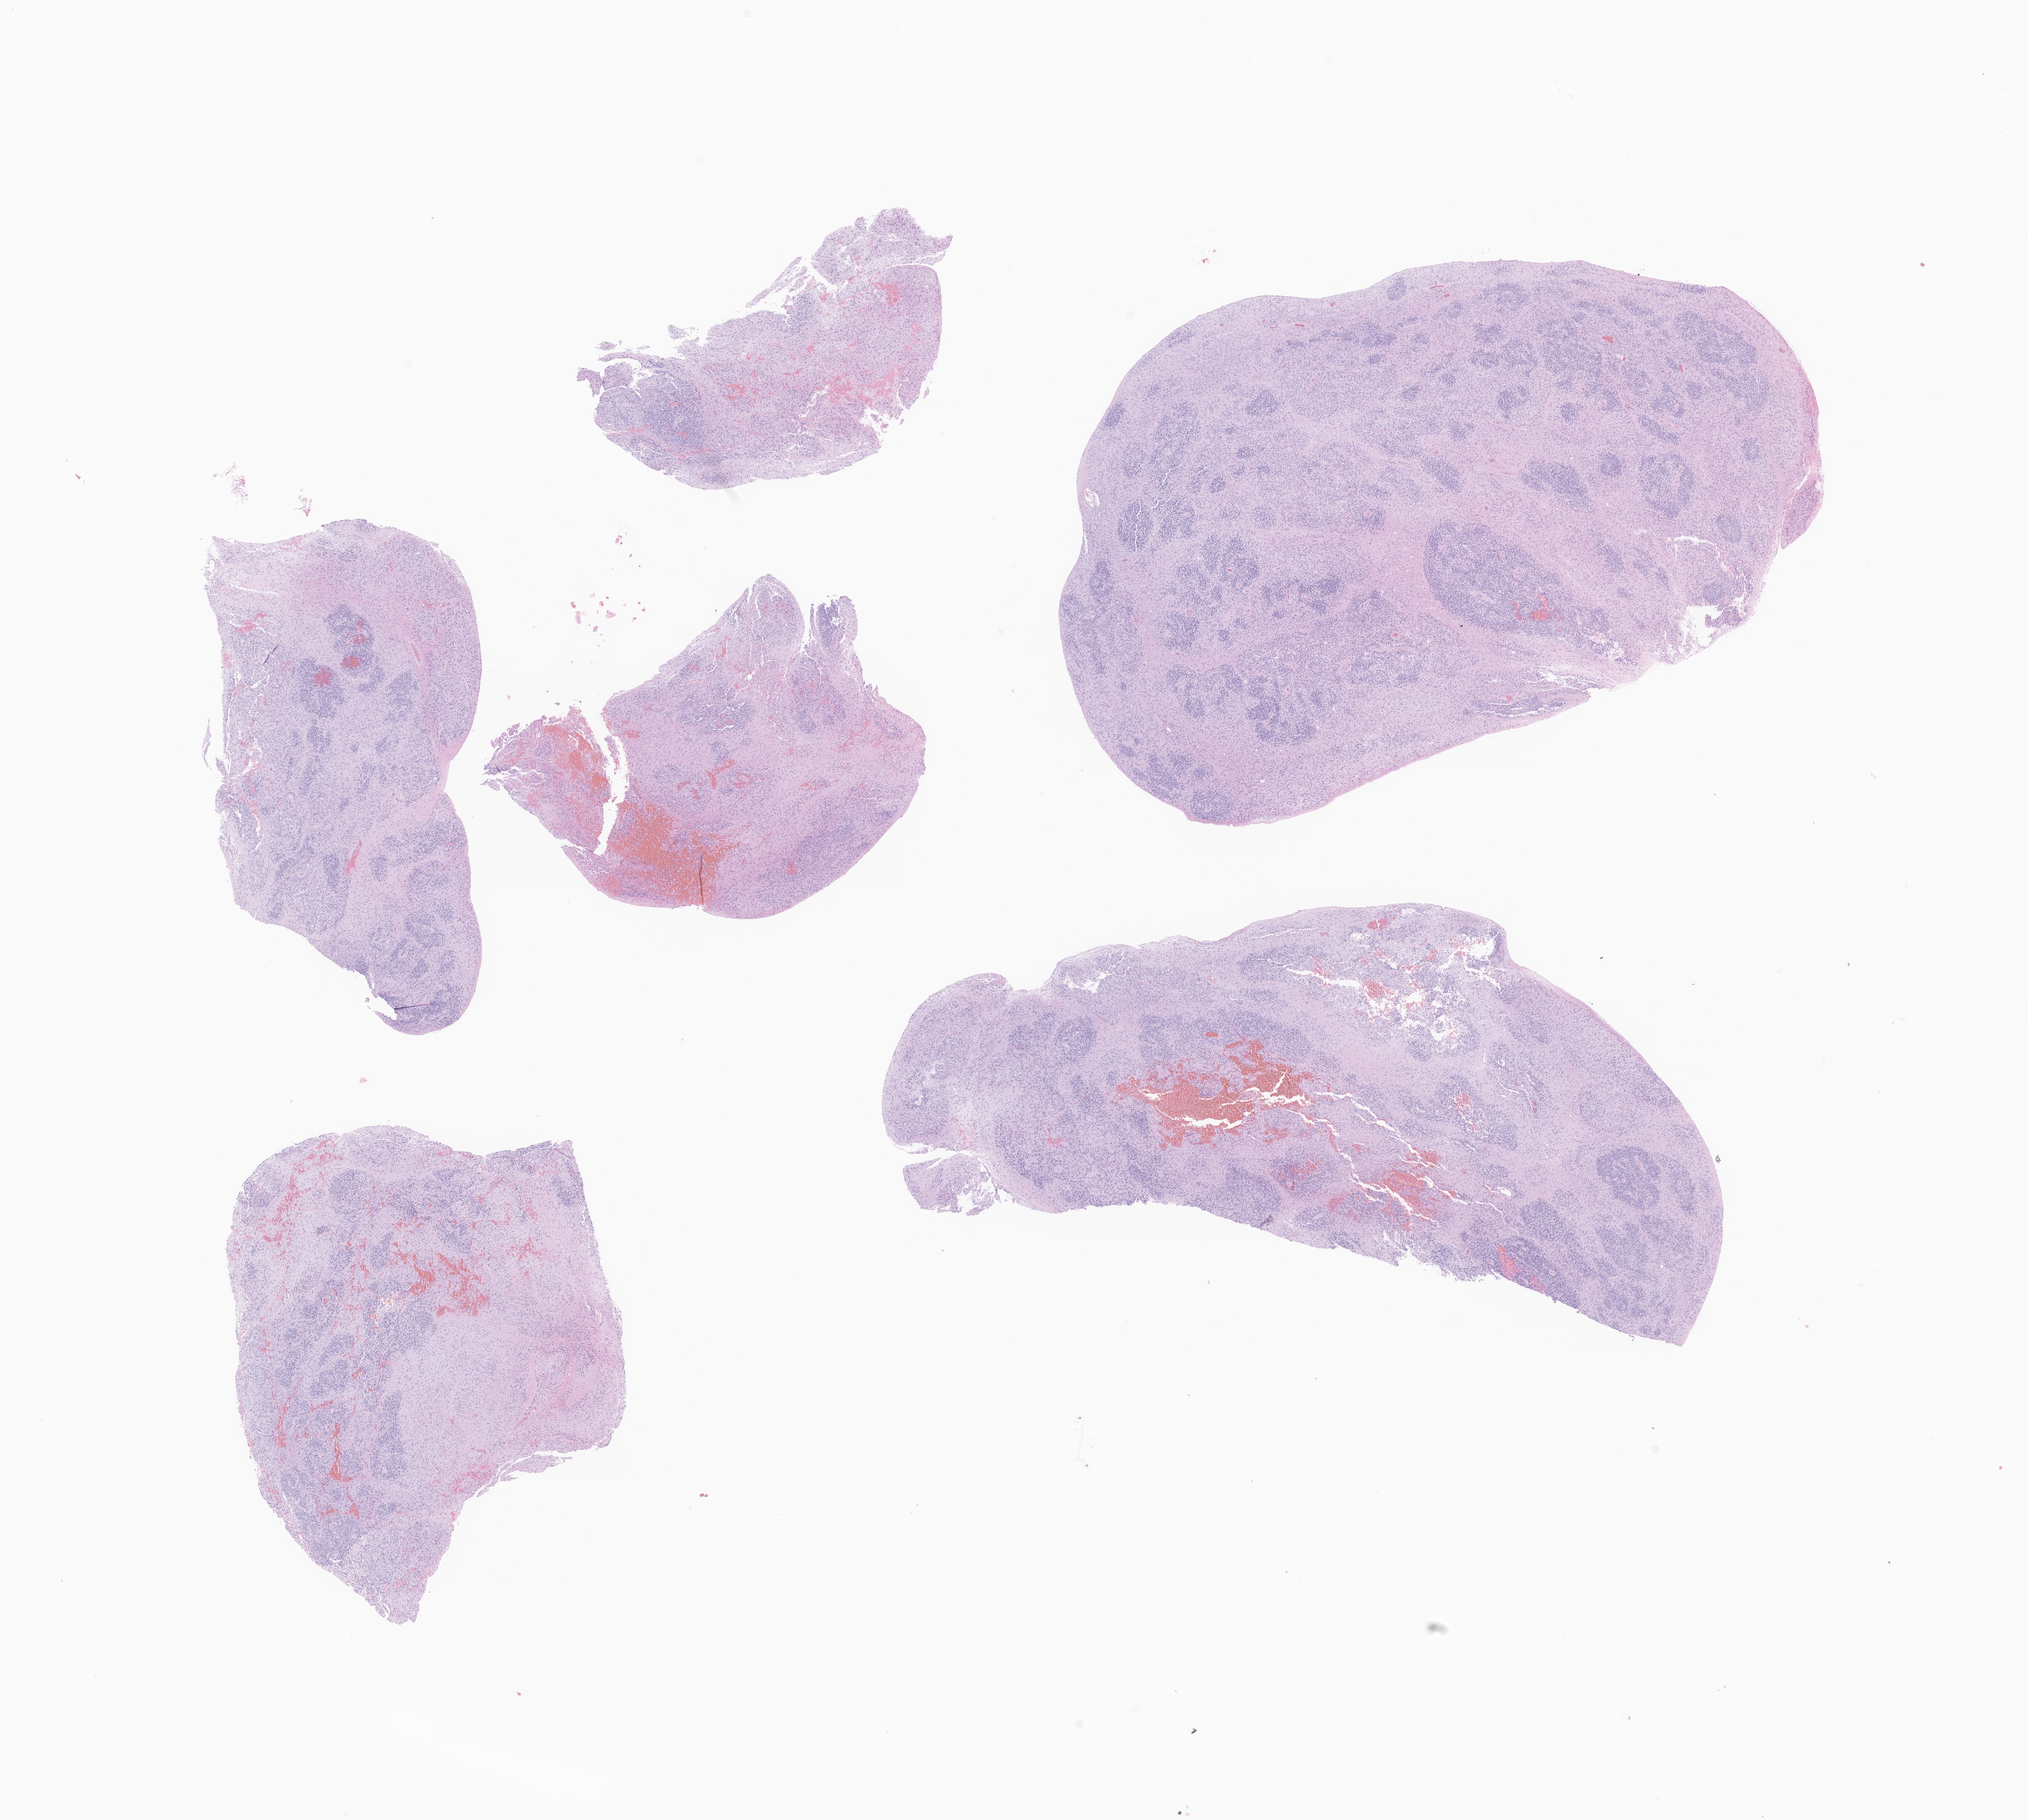
Whole-slide image, H&E stain of tumor tissue from the brain stem, whole scanned area (about 18.4 x 16.5 mm) shown as a low-resolution overview; formalin-fixed paraffin-embedded section. Patient female; age 53 months (4 years 5 months).
Recorded diagnosis: Ependymoma, NOS.